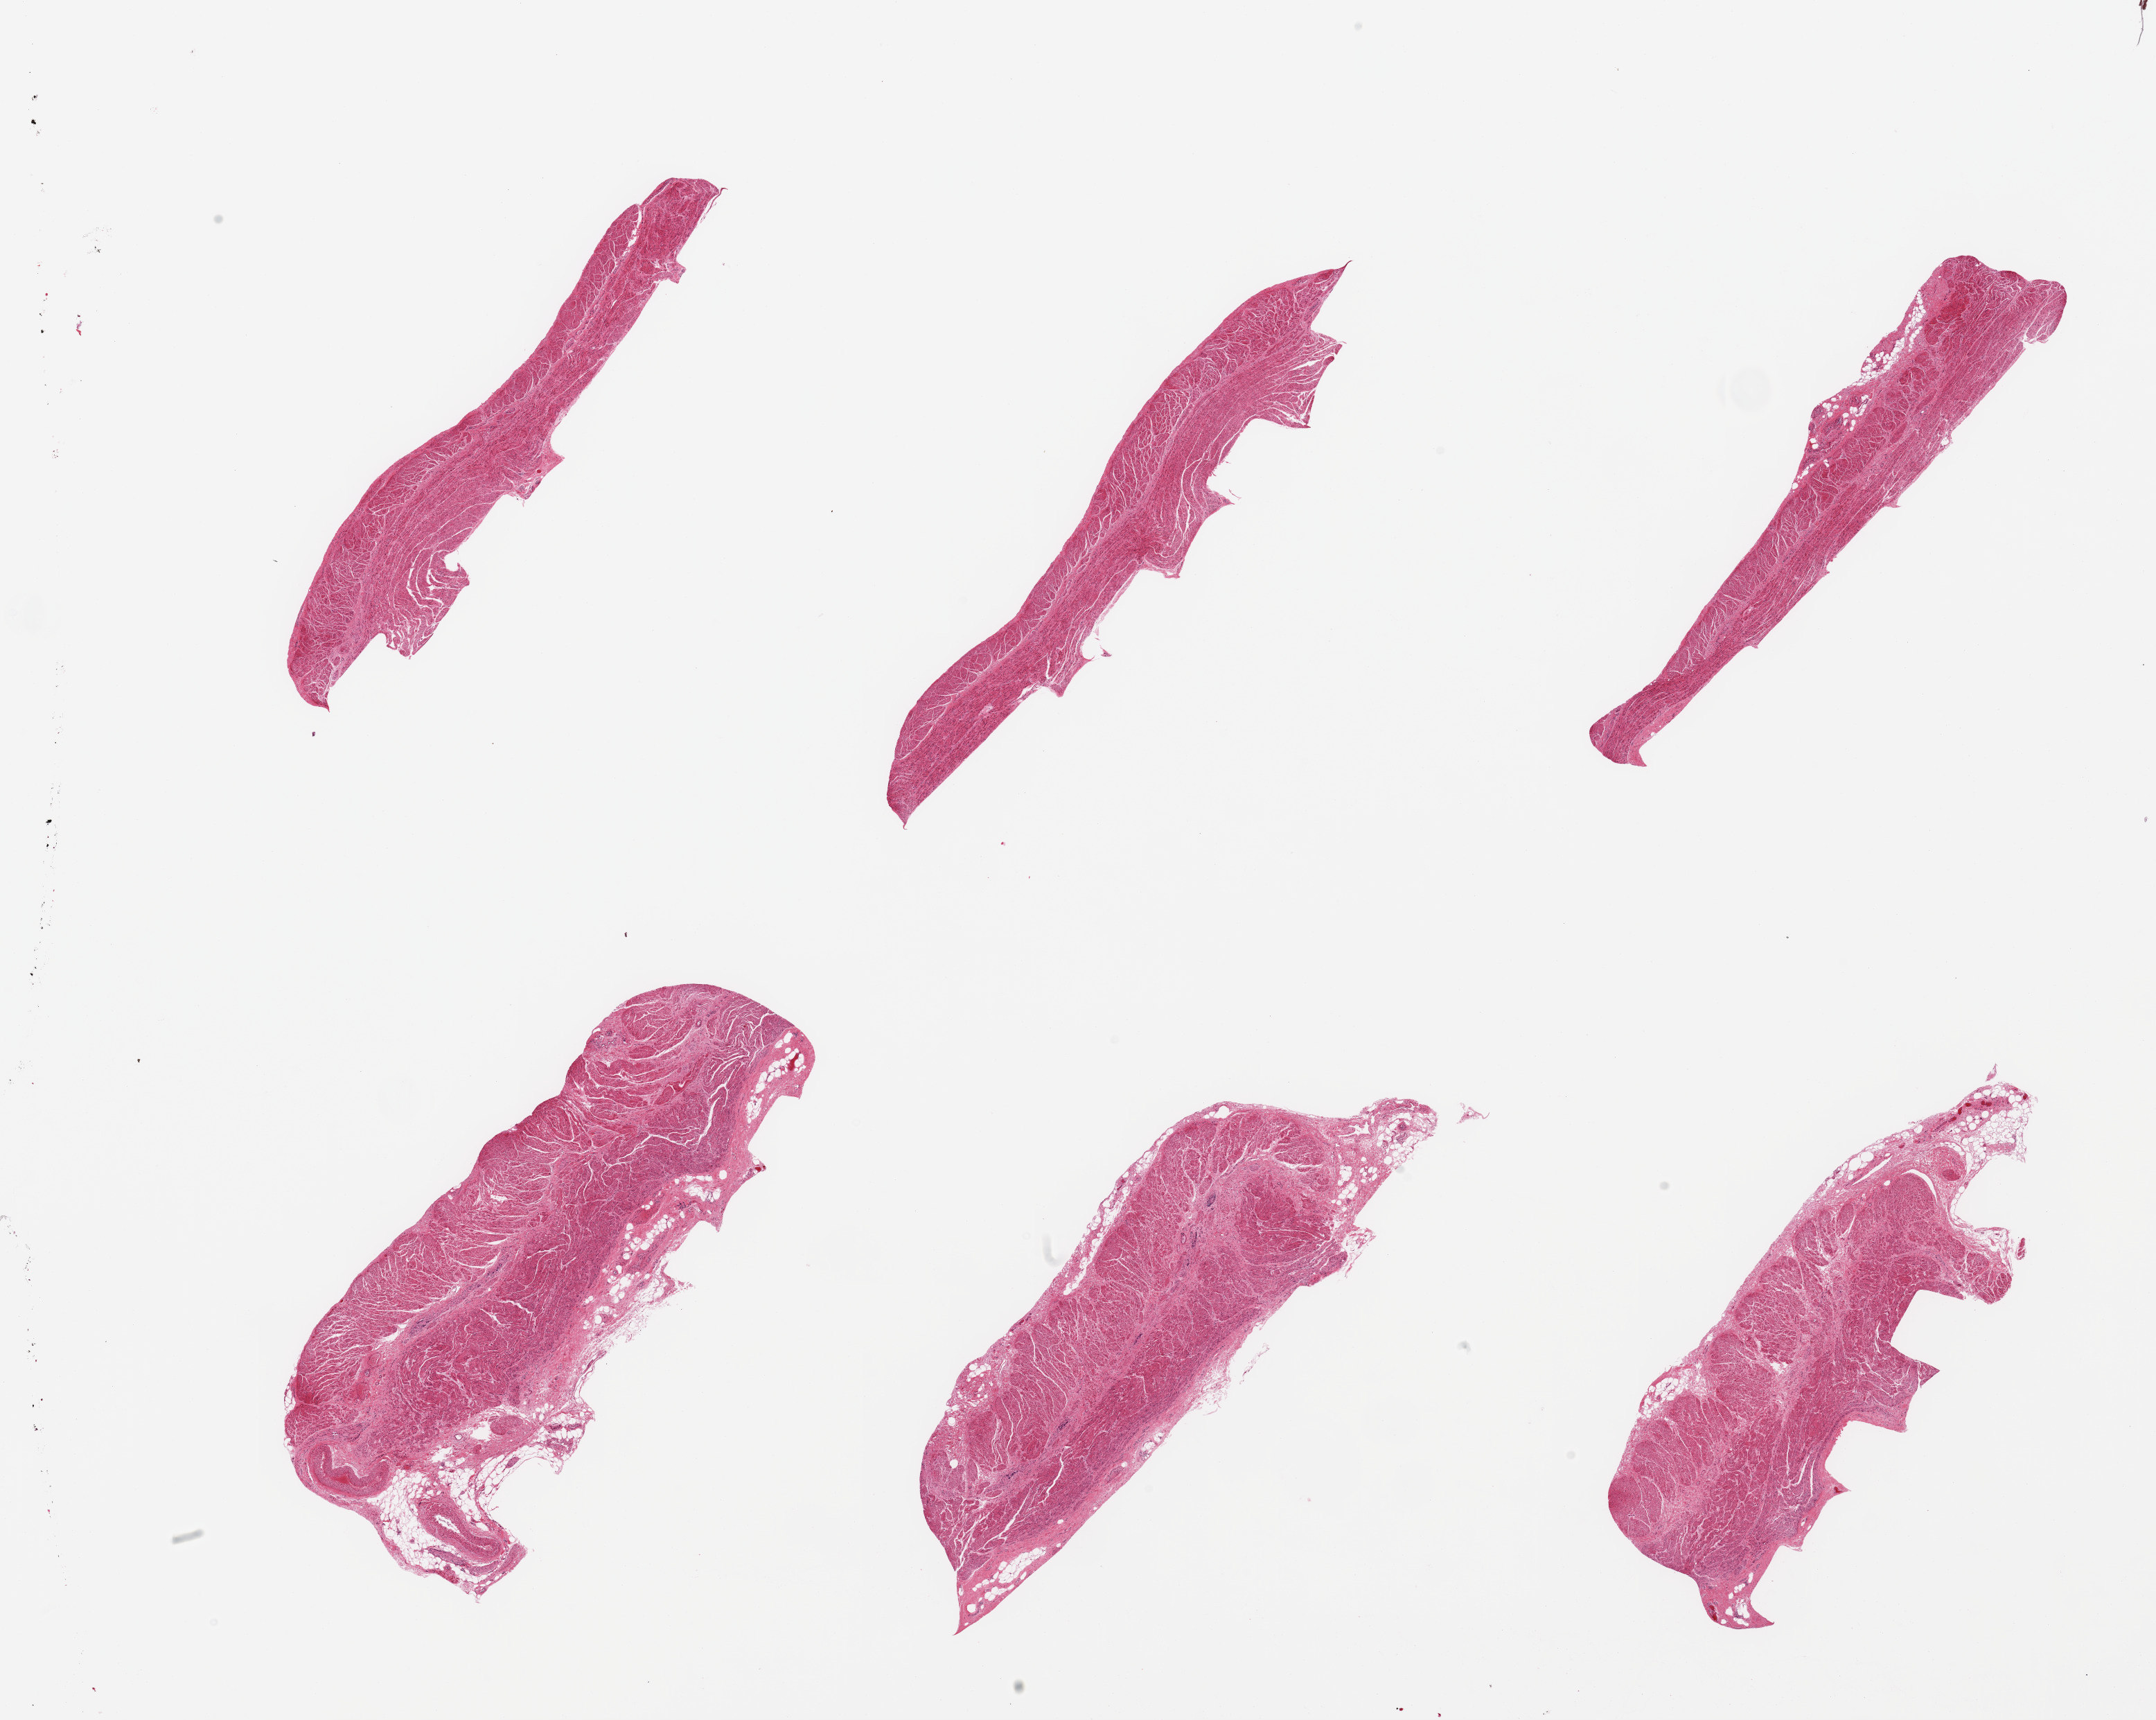
Digitized hematoxylin and eosin (H&E)-stained section, brightfield — low-resolution overview of the scanned area, about 24.6 x 19.6 mm; PAXgene-fixed, paraffin-embedded tissue; sampled site (target tissue): gastroesophageal junction; tissue donor sample.
Pathologist's review note for this sample: 6 pieces, confirmed target muscularis; focal adherent serosal fat up to ~1.6mm.